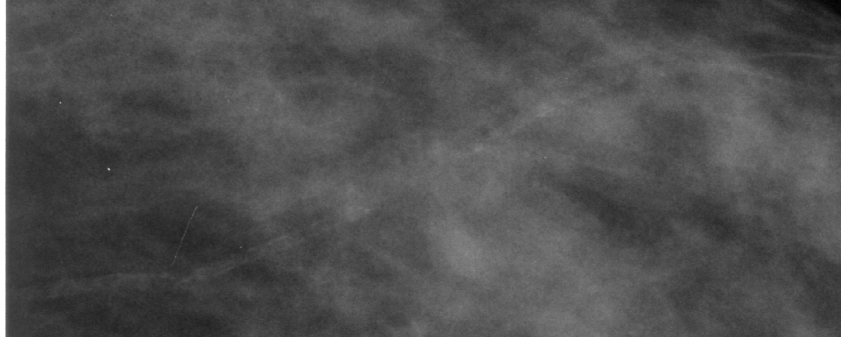
Cropped region of a digitized screen-film mammogram centred on a radiologist-marked abnormality; left breast; CC view; BI-RADS breast density category 3 (scale 1–4).
Finding: calcifications, morphology vascular; BI-RADS assessment category 2; benign without callback (not worked up further).